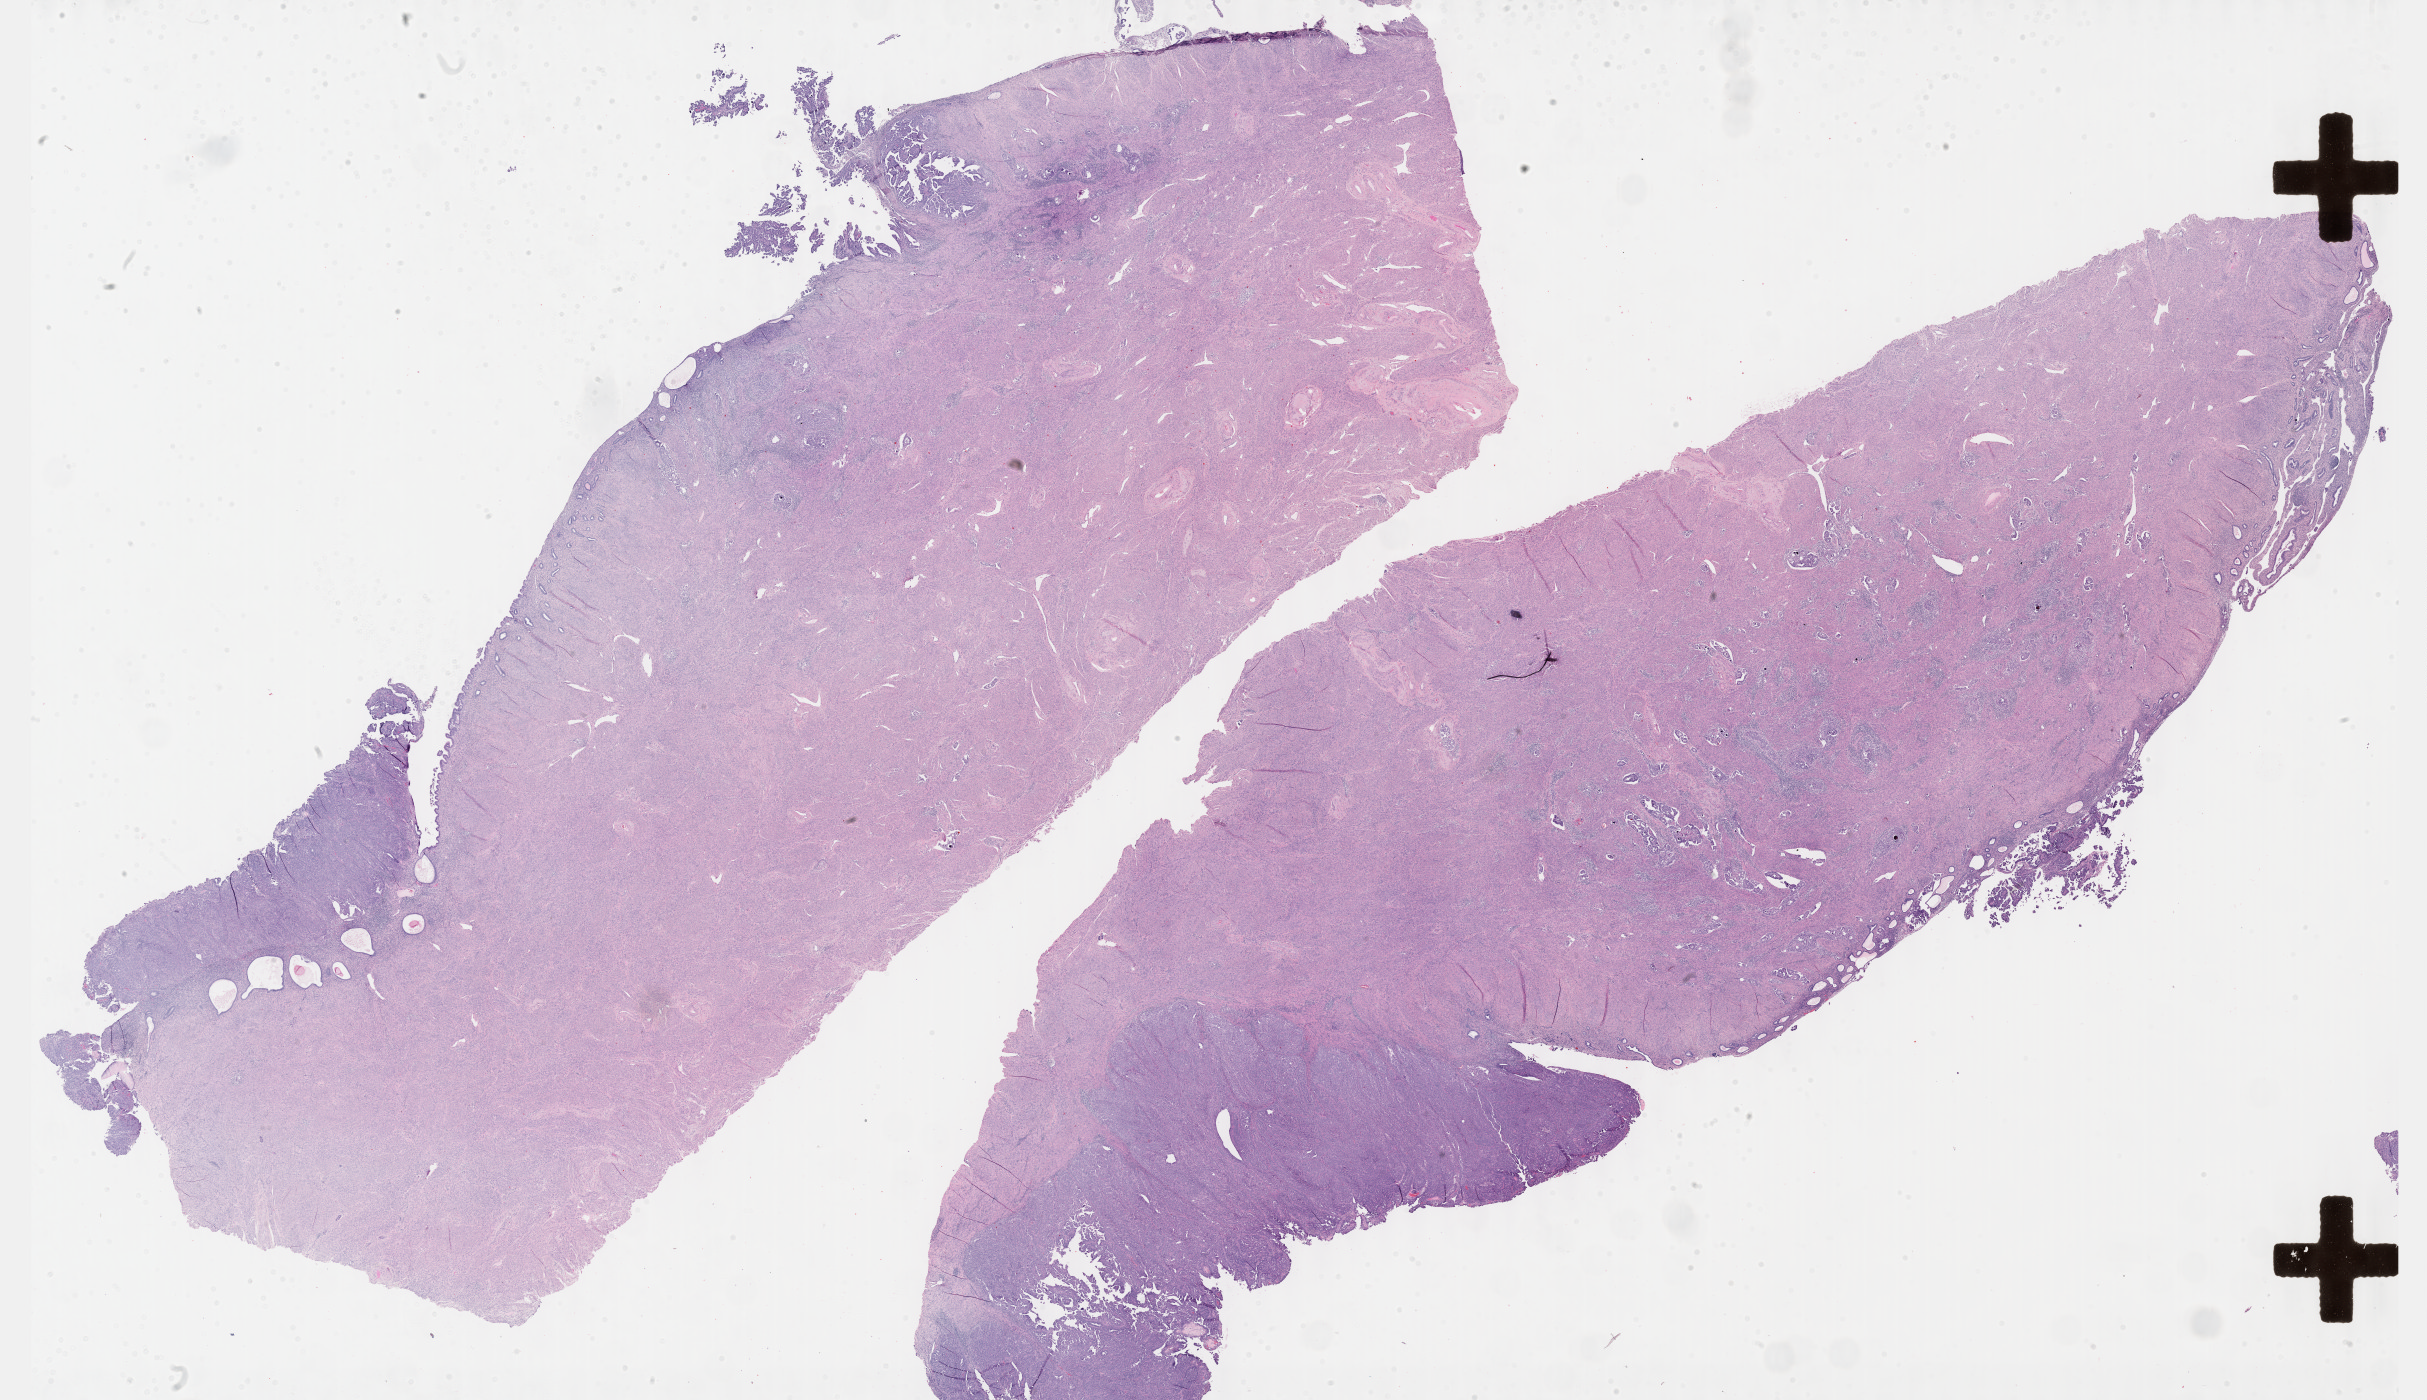
H&E whole-slide image, shown as a low-resolution overview of the whole scanned area (about 39.2 x 22.6 mm); formalin-fixed paraffin-embedded (FFPE) diagnostic section; uterus, primary tumour sample. Female patient; age at initial diagnosis 73 years. Histologic grade: G3 (poorly differentiated).
Pathologic diagnosis: Serous surface papillary carcinoma (endometrium). FIGO stage: IA.